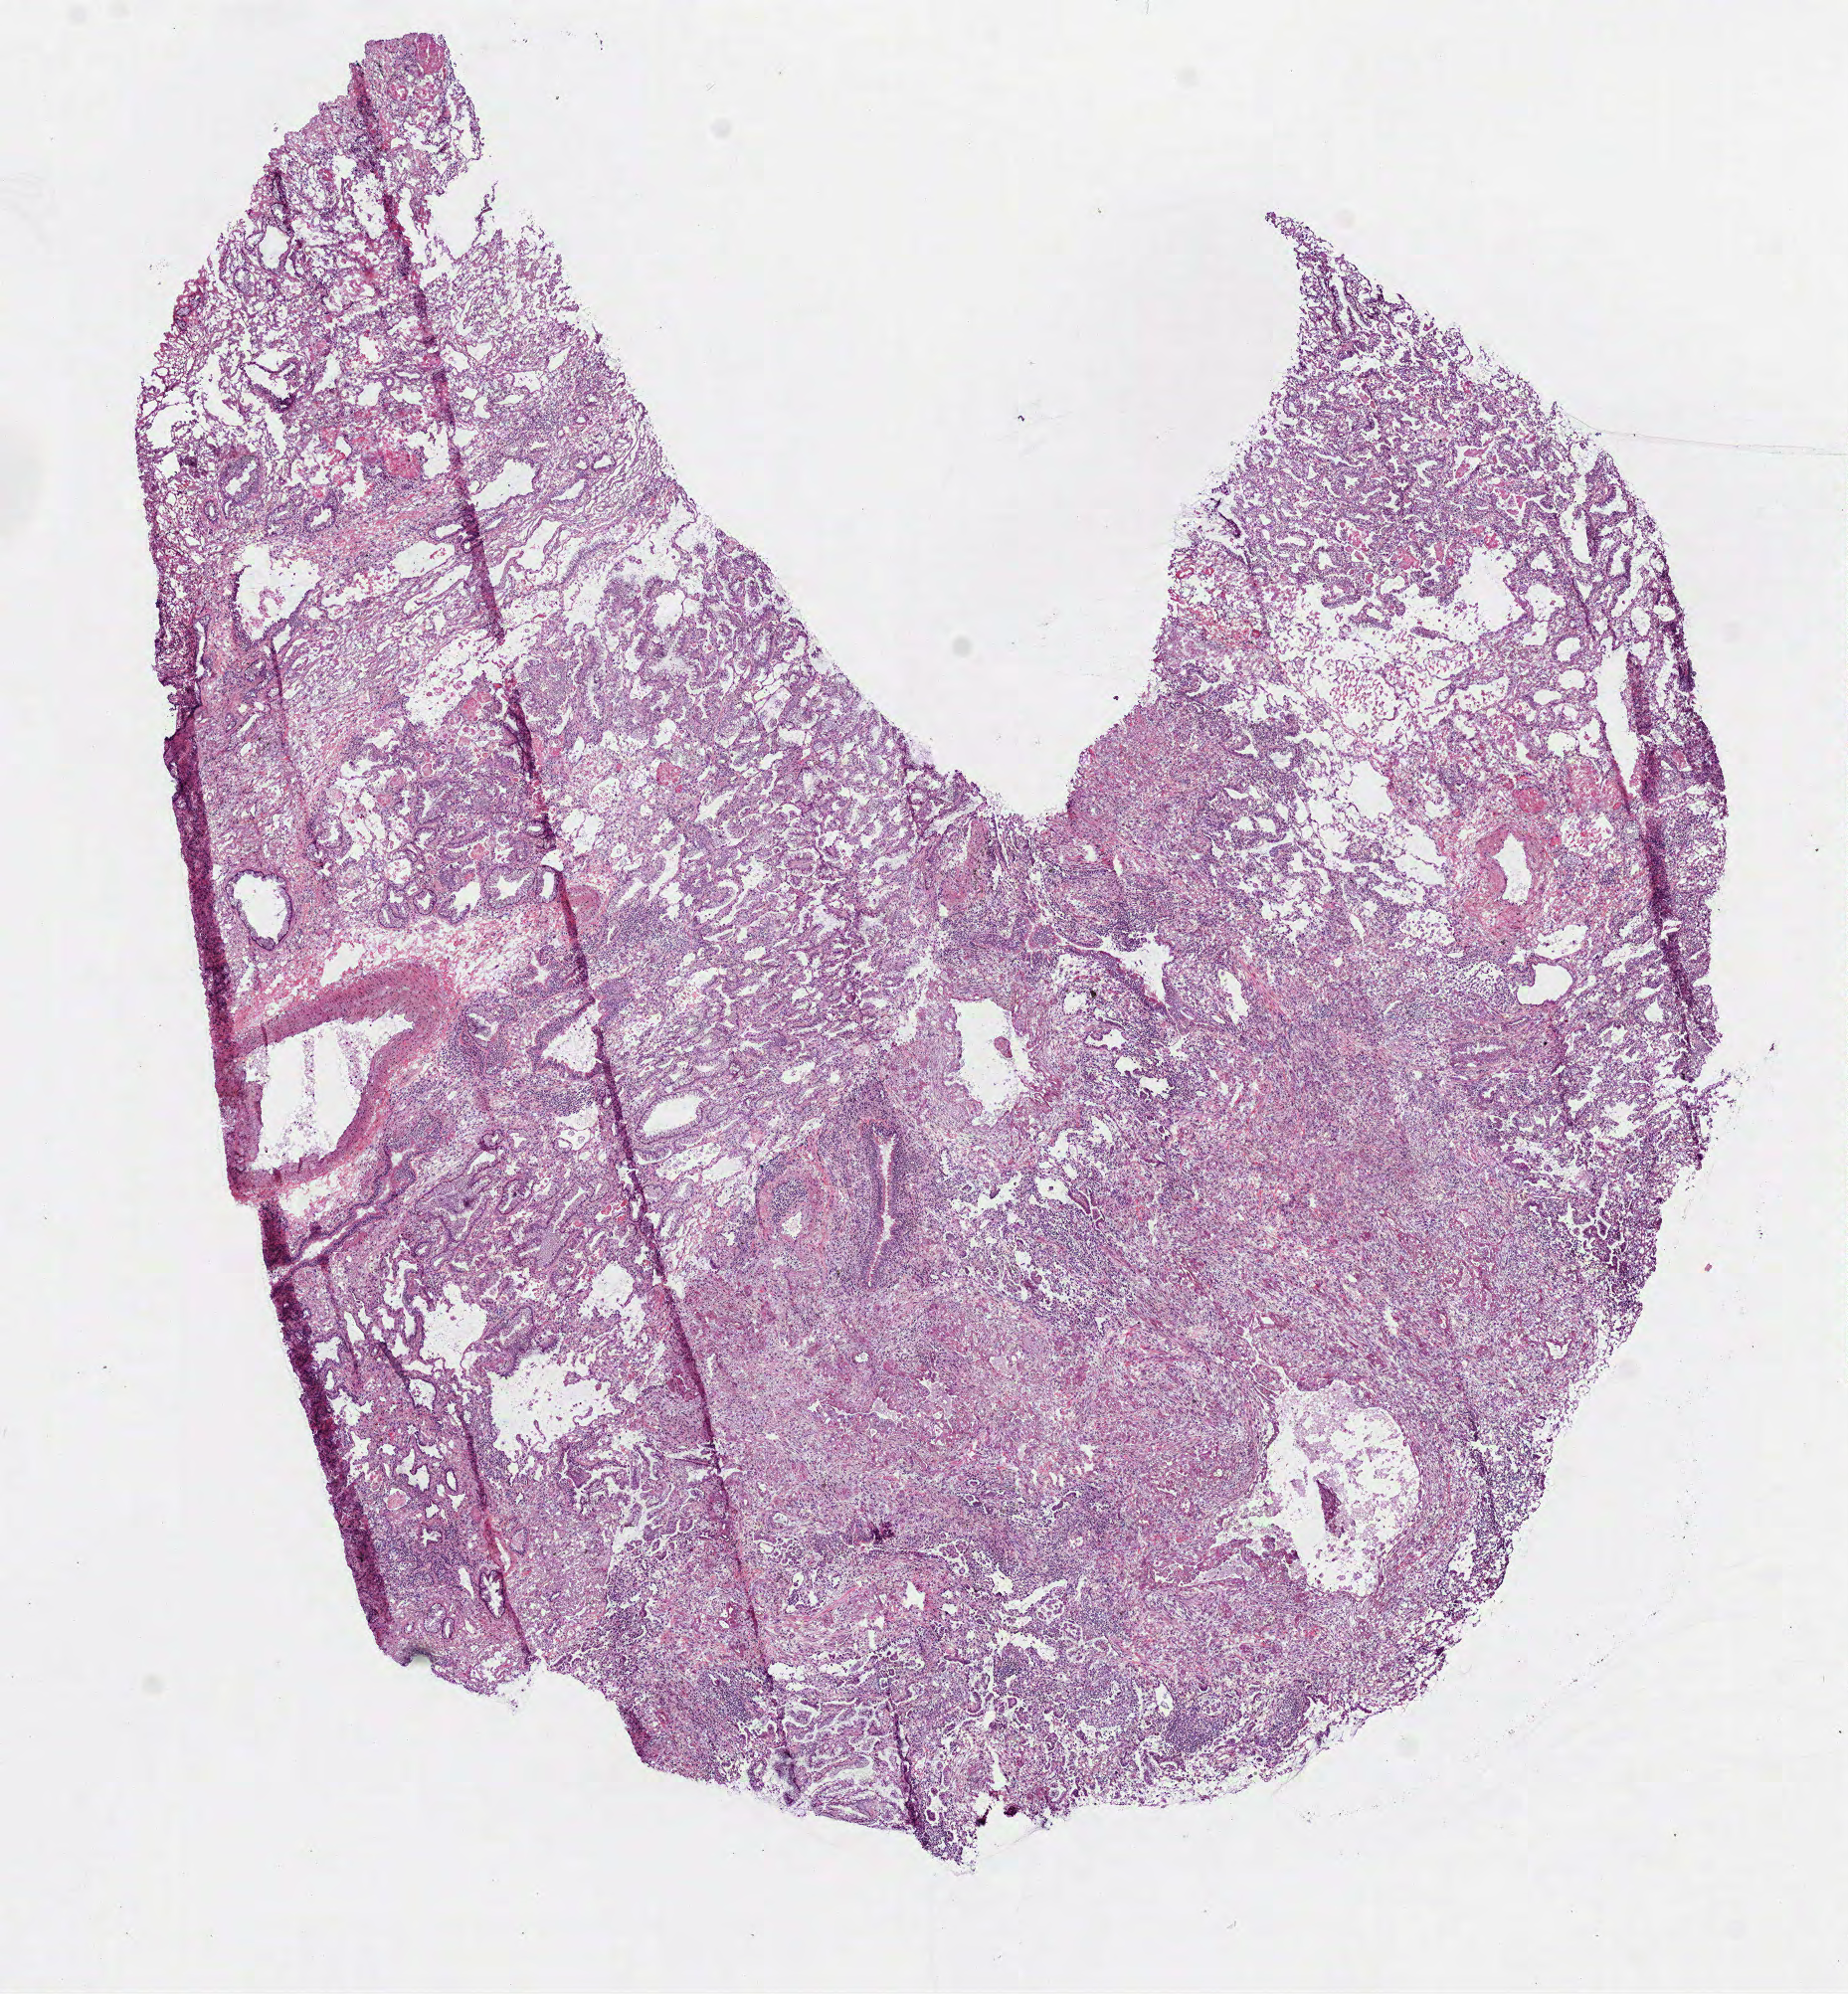
Whole-slide histology image, Hematoxylin and eosin (H&E) stained — a low-resolution overview of the entire scanned area, about 7.5 x 8.1 mm. Frozen section from the top of the tissue portion. Sample: primary tumour, lung. Male patient. Slide review estimates, as recorded: tumour cells 60%, tumour nuclei 60%, normal cells 20%, stromal cells 15%, necrosis 5%.
Histologic diagnosis: Adenocarcinoma, NOS. Laterality: right. AJCC pathologic stage: IIB (6th edition).